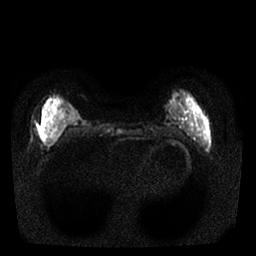
Breast MRI, one axial slice; slice 5 of 25 in the series (ordered by position); diffusion-weighted series; image 2 of 4 stored at this slice position (different b-values; order by instance number); 1.5 T; 4 mm slice thickness; 256 × 256 image matrix, field of view 310 × 310 mm. Female patient.
Outlined on this slice (expert manual segmentation):
- tumour on diffusion-weighted imaging: bounding box (x1, y1, x2, y2) in pixels: (41, 123, 45, 128)